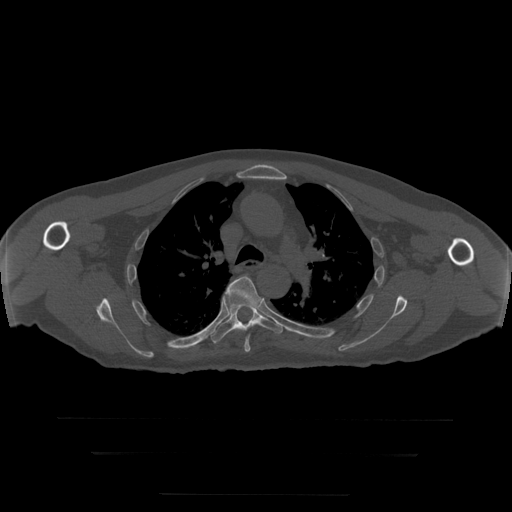
CT including the spine, one axial slice. Slice 215 of 397 in the series (ordered by position). Reconstruction kernel STANDARD. Bone window (W 1800 / L 400 HU). 1.25 mm slice thickness. 512 × 512 image matrix. Patient age 73 years. Case-level facts recorded for this patient, not image findings: primary cancer: prostate.
Structures marked on this image (semi-automatically segmented with operator editing):
- T5 vertebra: bounding box <226,276,261,353> (left, top, right, bottom; pixels)
- T6 vertebra: <206,296,283,344>